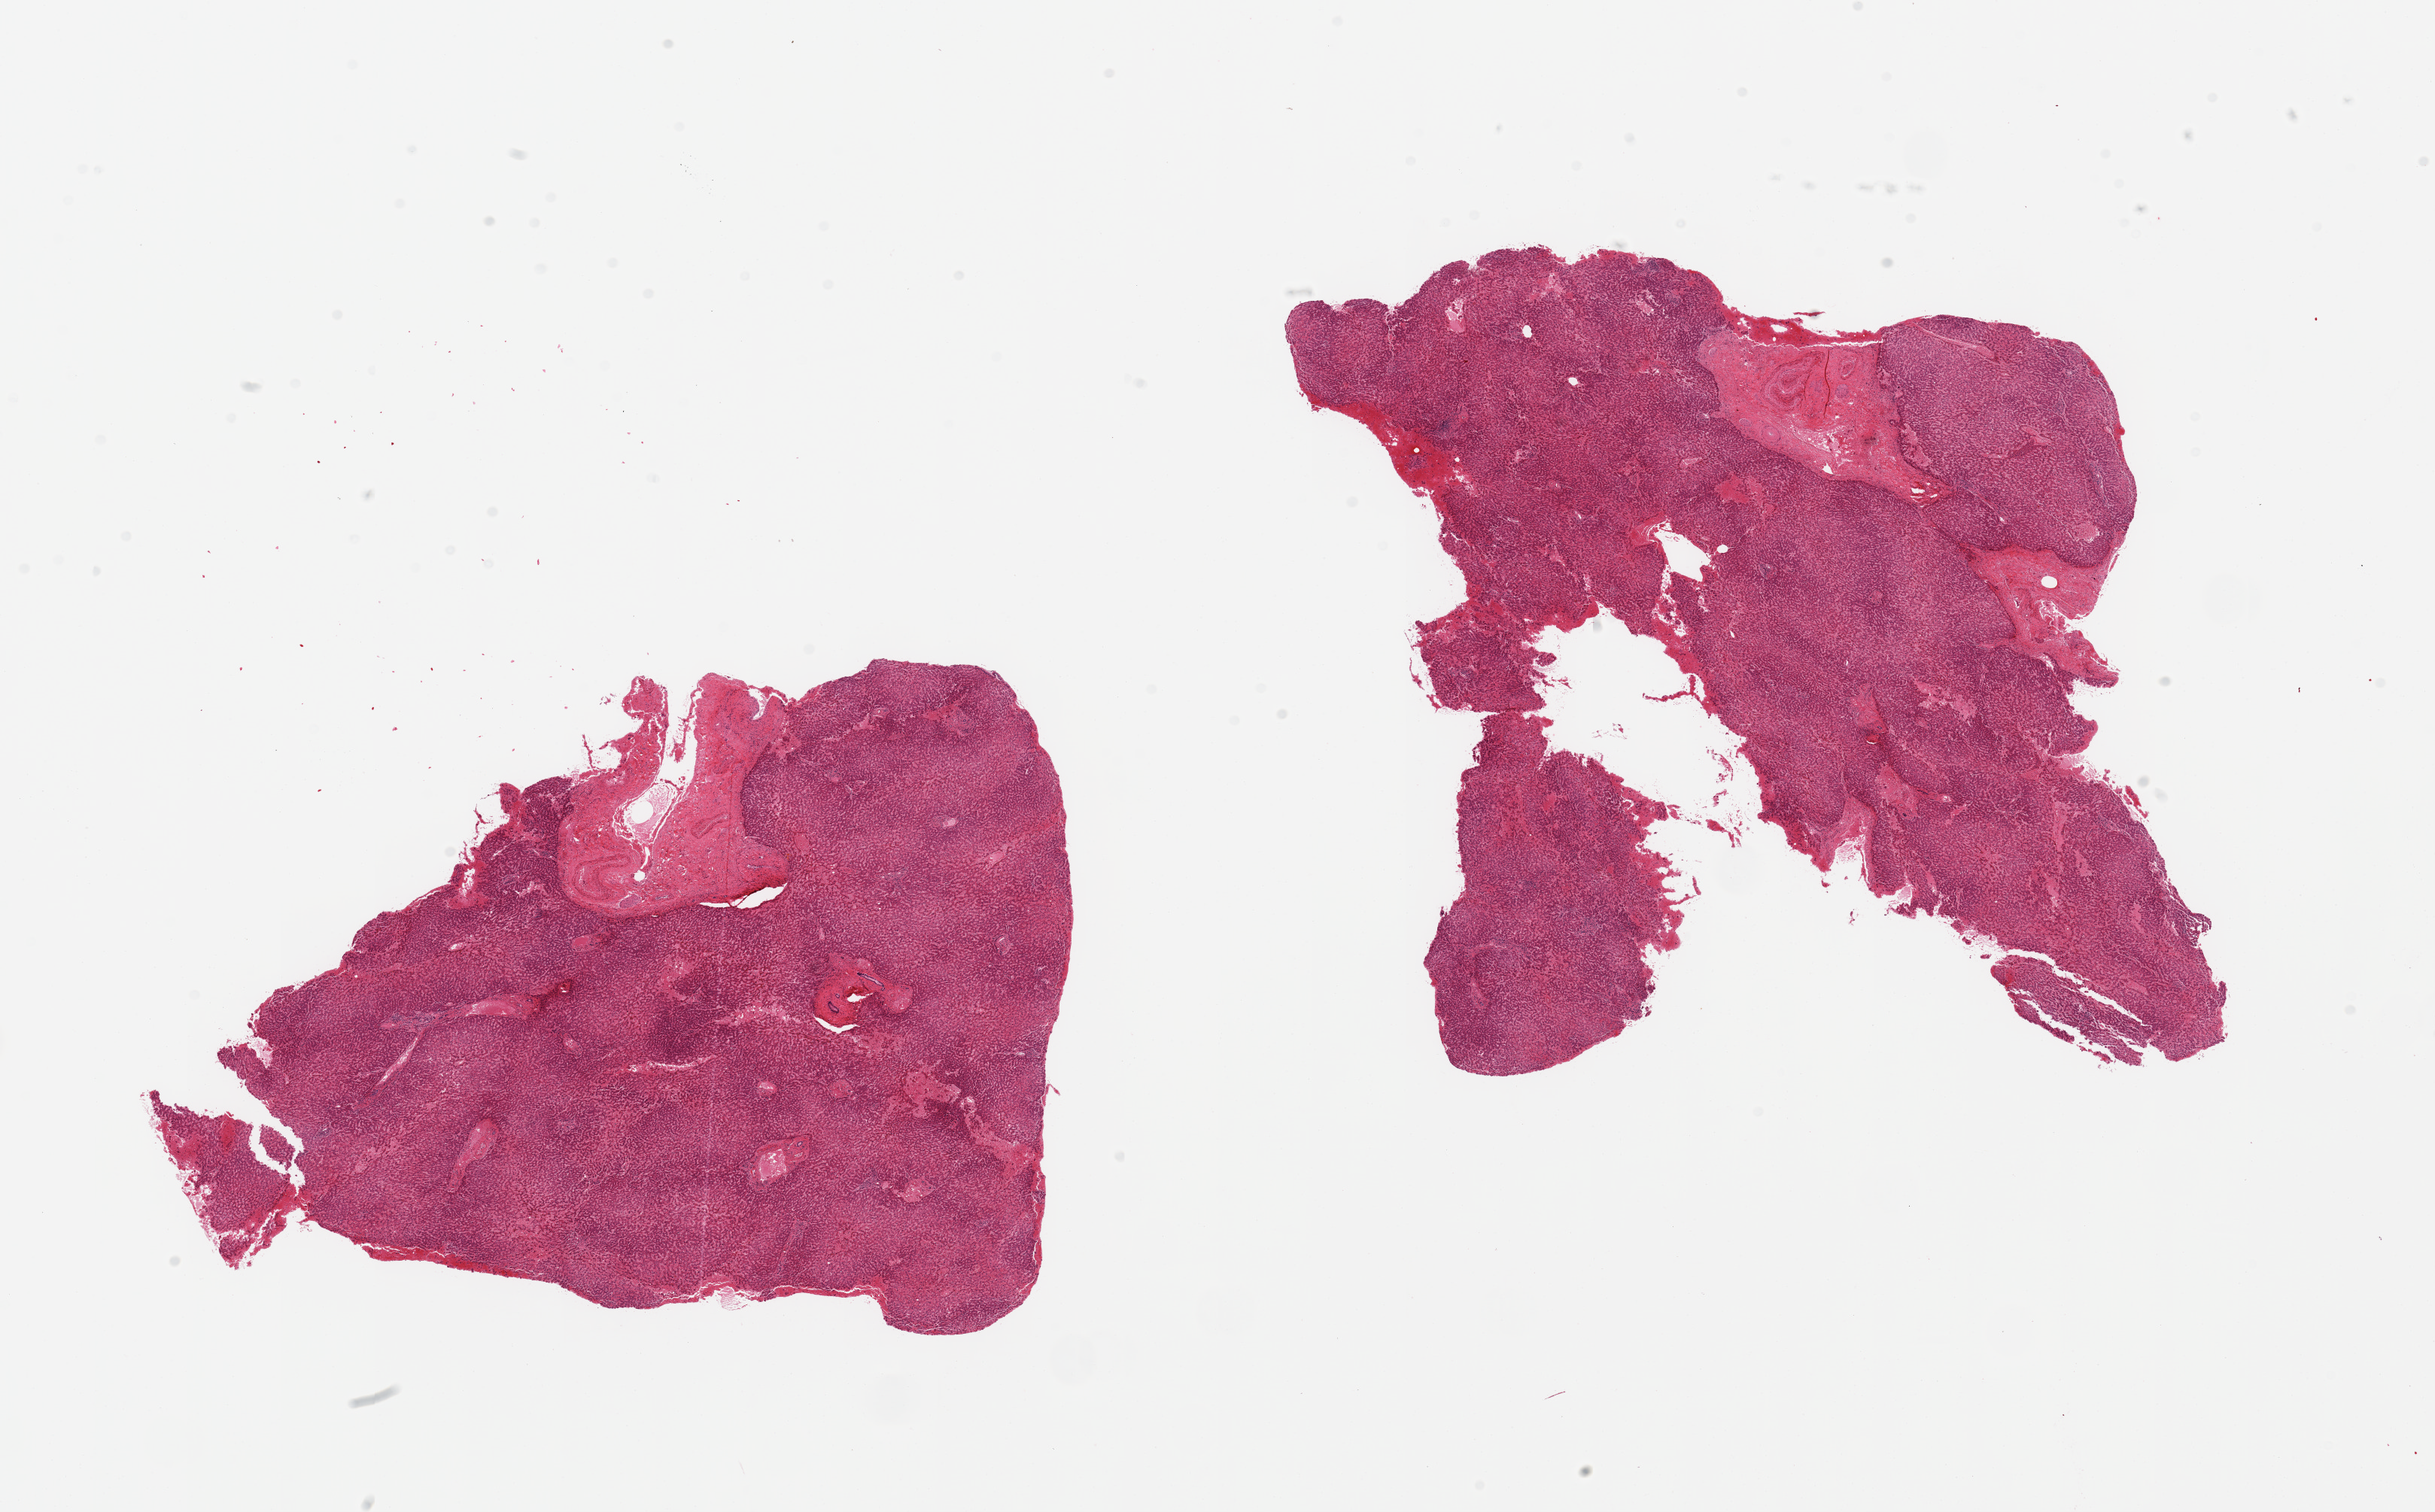
Hematoxylin and eosin (H&E) whole-slide image, whole scanned area (about 25.6 x 15.9 mm) shown as a low-resolution overview, PAXgene-fixed, paraffin-embedded tissue, section of liver (target tissue), tissue donor sample. Female donor.
Reviewer comment on this tissue sample: 2 pieces; congested with focal hemorrhages; large vessels comprise 10%; no fat, no cirrhosis.